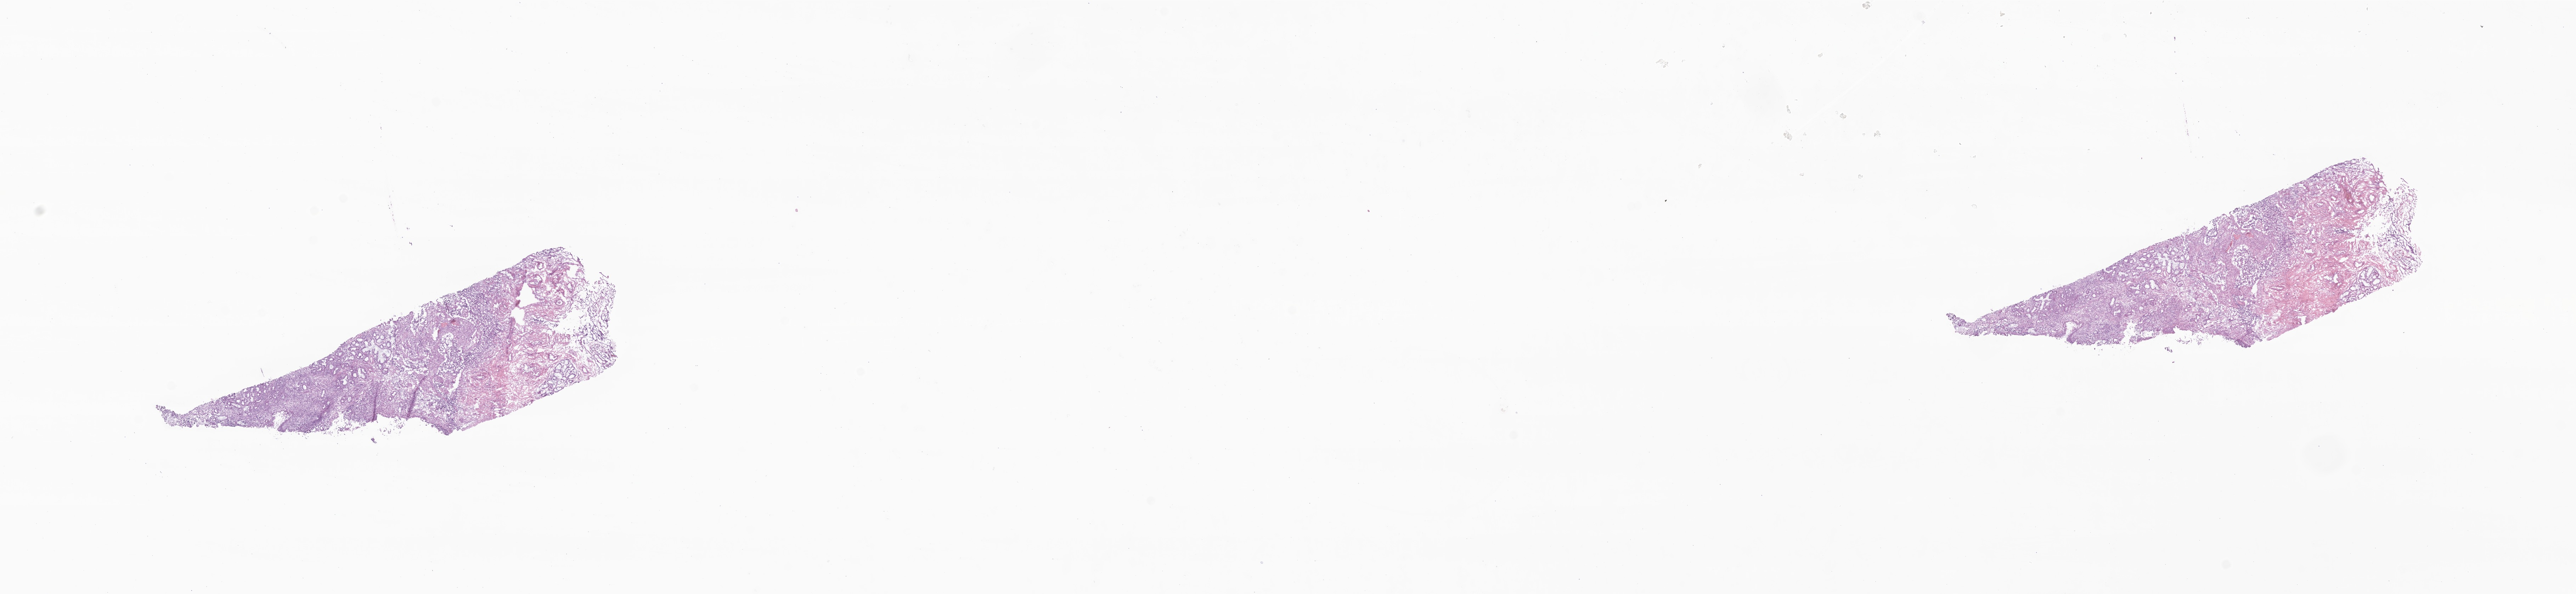
Digitized hematoxylin and eosin (H&E)-stained section of tumor tissue from the nasal cavity — shown as a low-resolution overview of the whole scanned area (about 30.7 x 7.1 mm); frozen section. Female patient, age 193 months (16 years 1 month).
* diagnosis (ICD-O-3 morphology term): Alveolar rhabdomyosarcoma